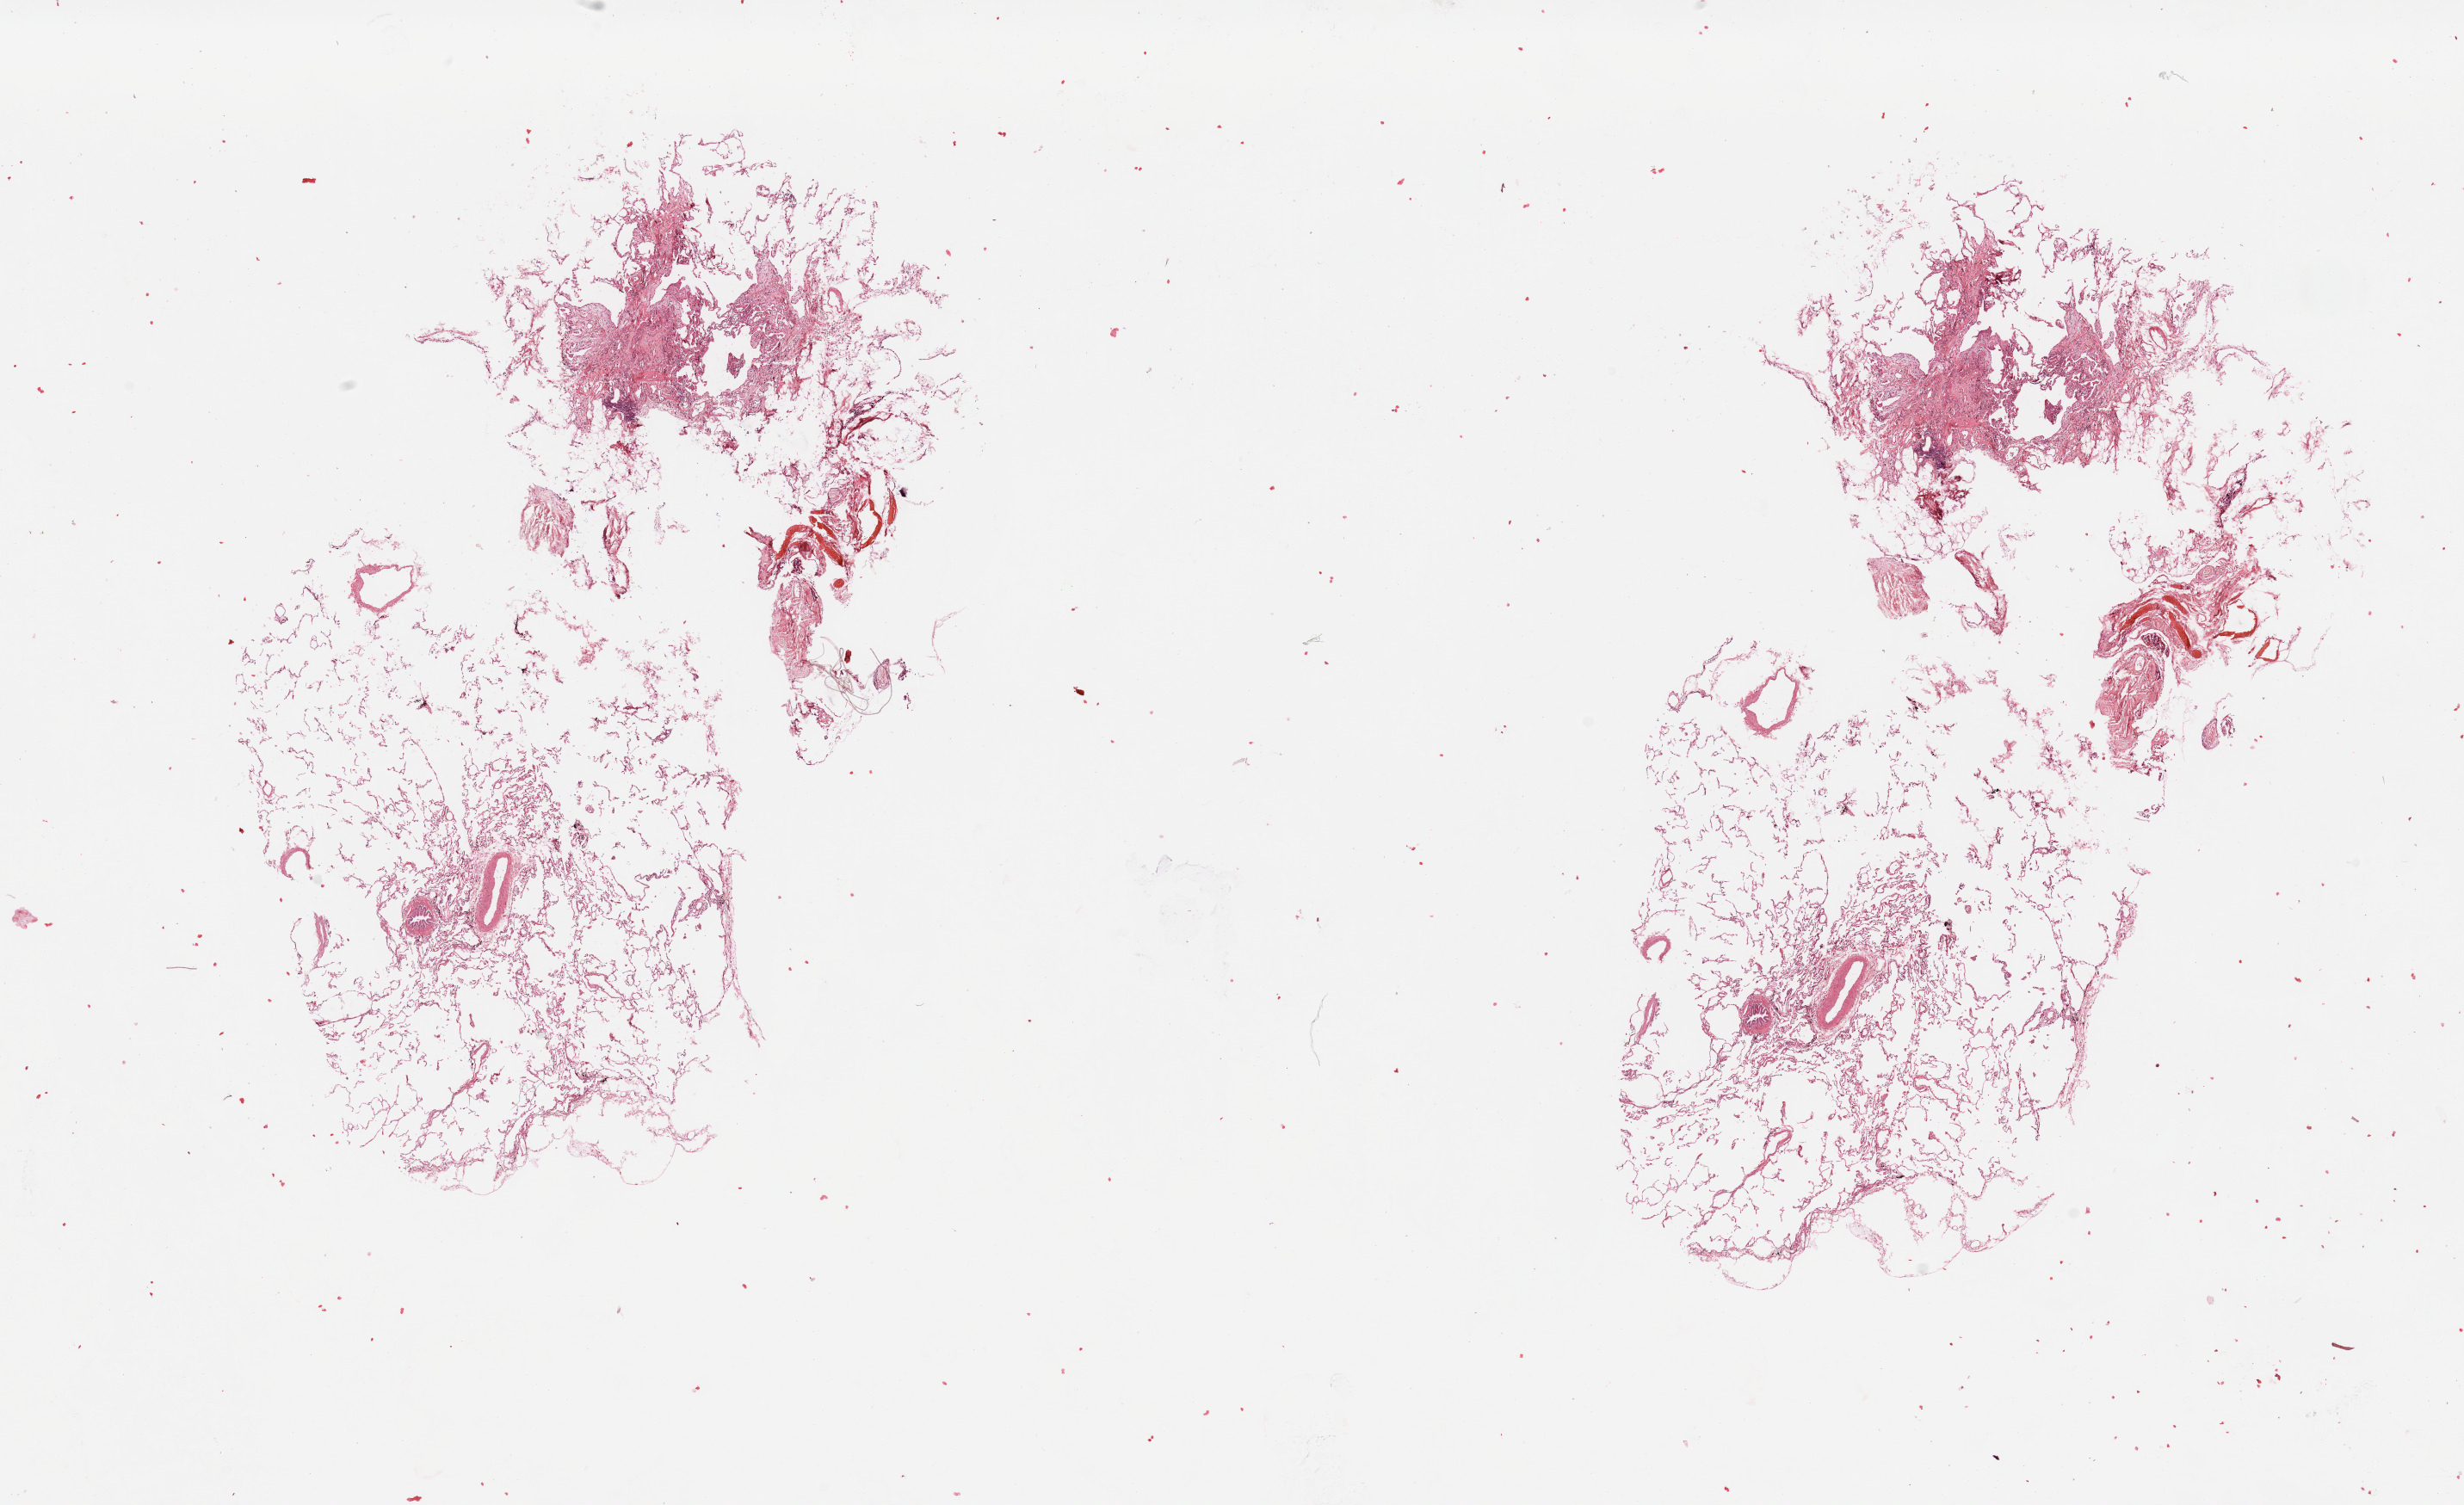
Digitized H&E-stained tissue section (whole slide), shown as a low-resolution overview of the whole scanned area (about 22.6 x 13.8 mm), normal (non-tumour) tissue sample, sampled site: lung. Patient: male, age 69 years.
This section: normal (non-tumour) tissue from the same patient. Patient diagnosis: Squamous cell carcinoma, NOS.